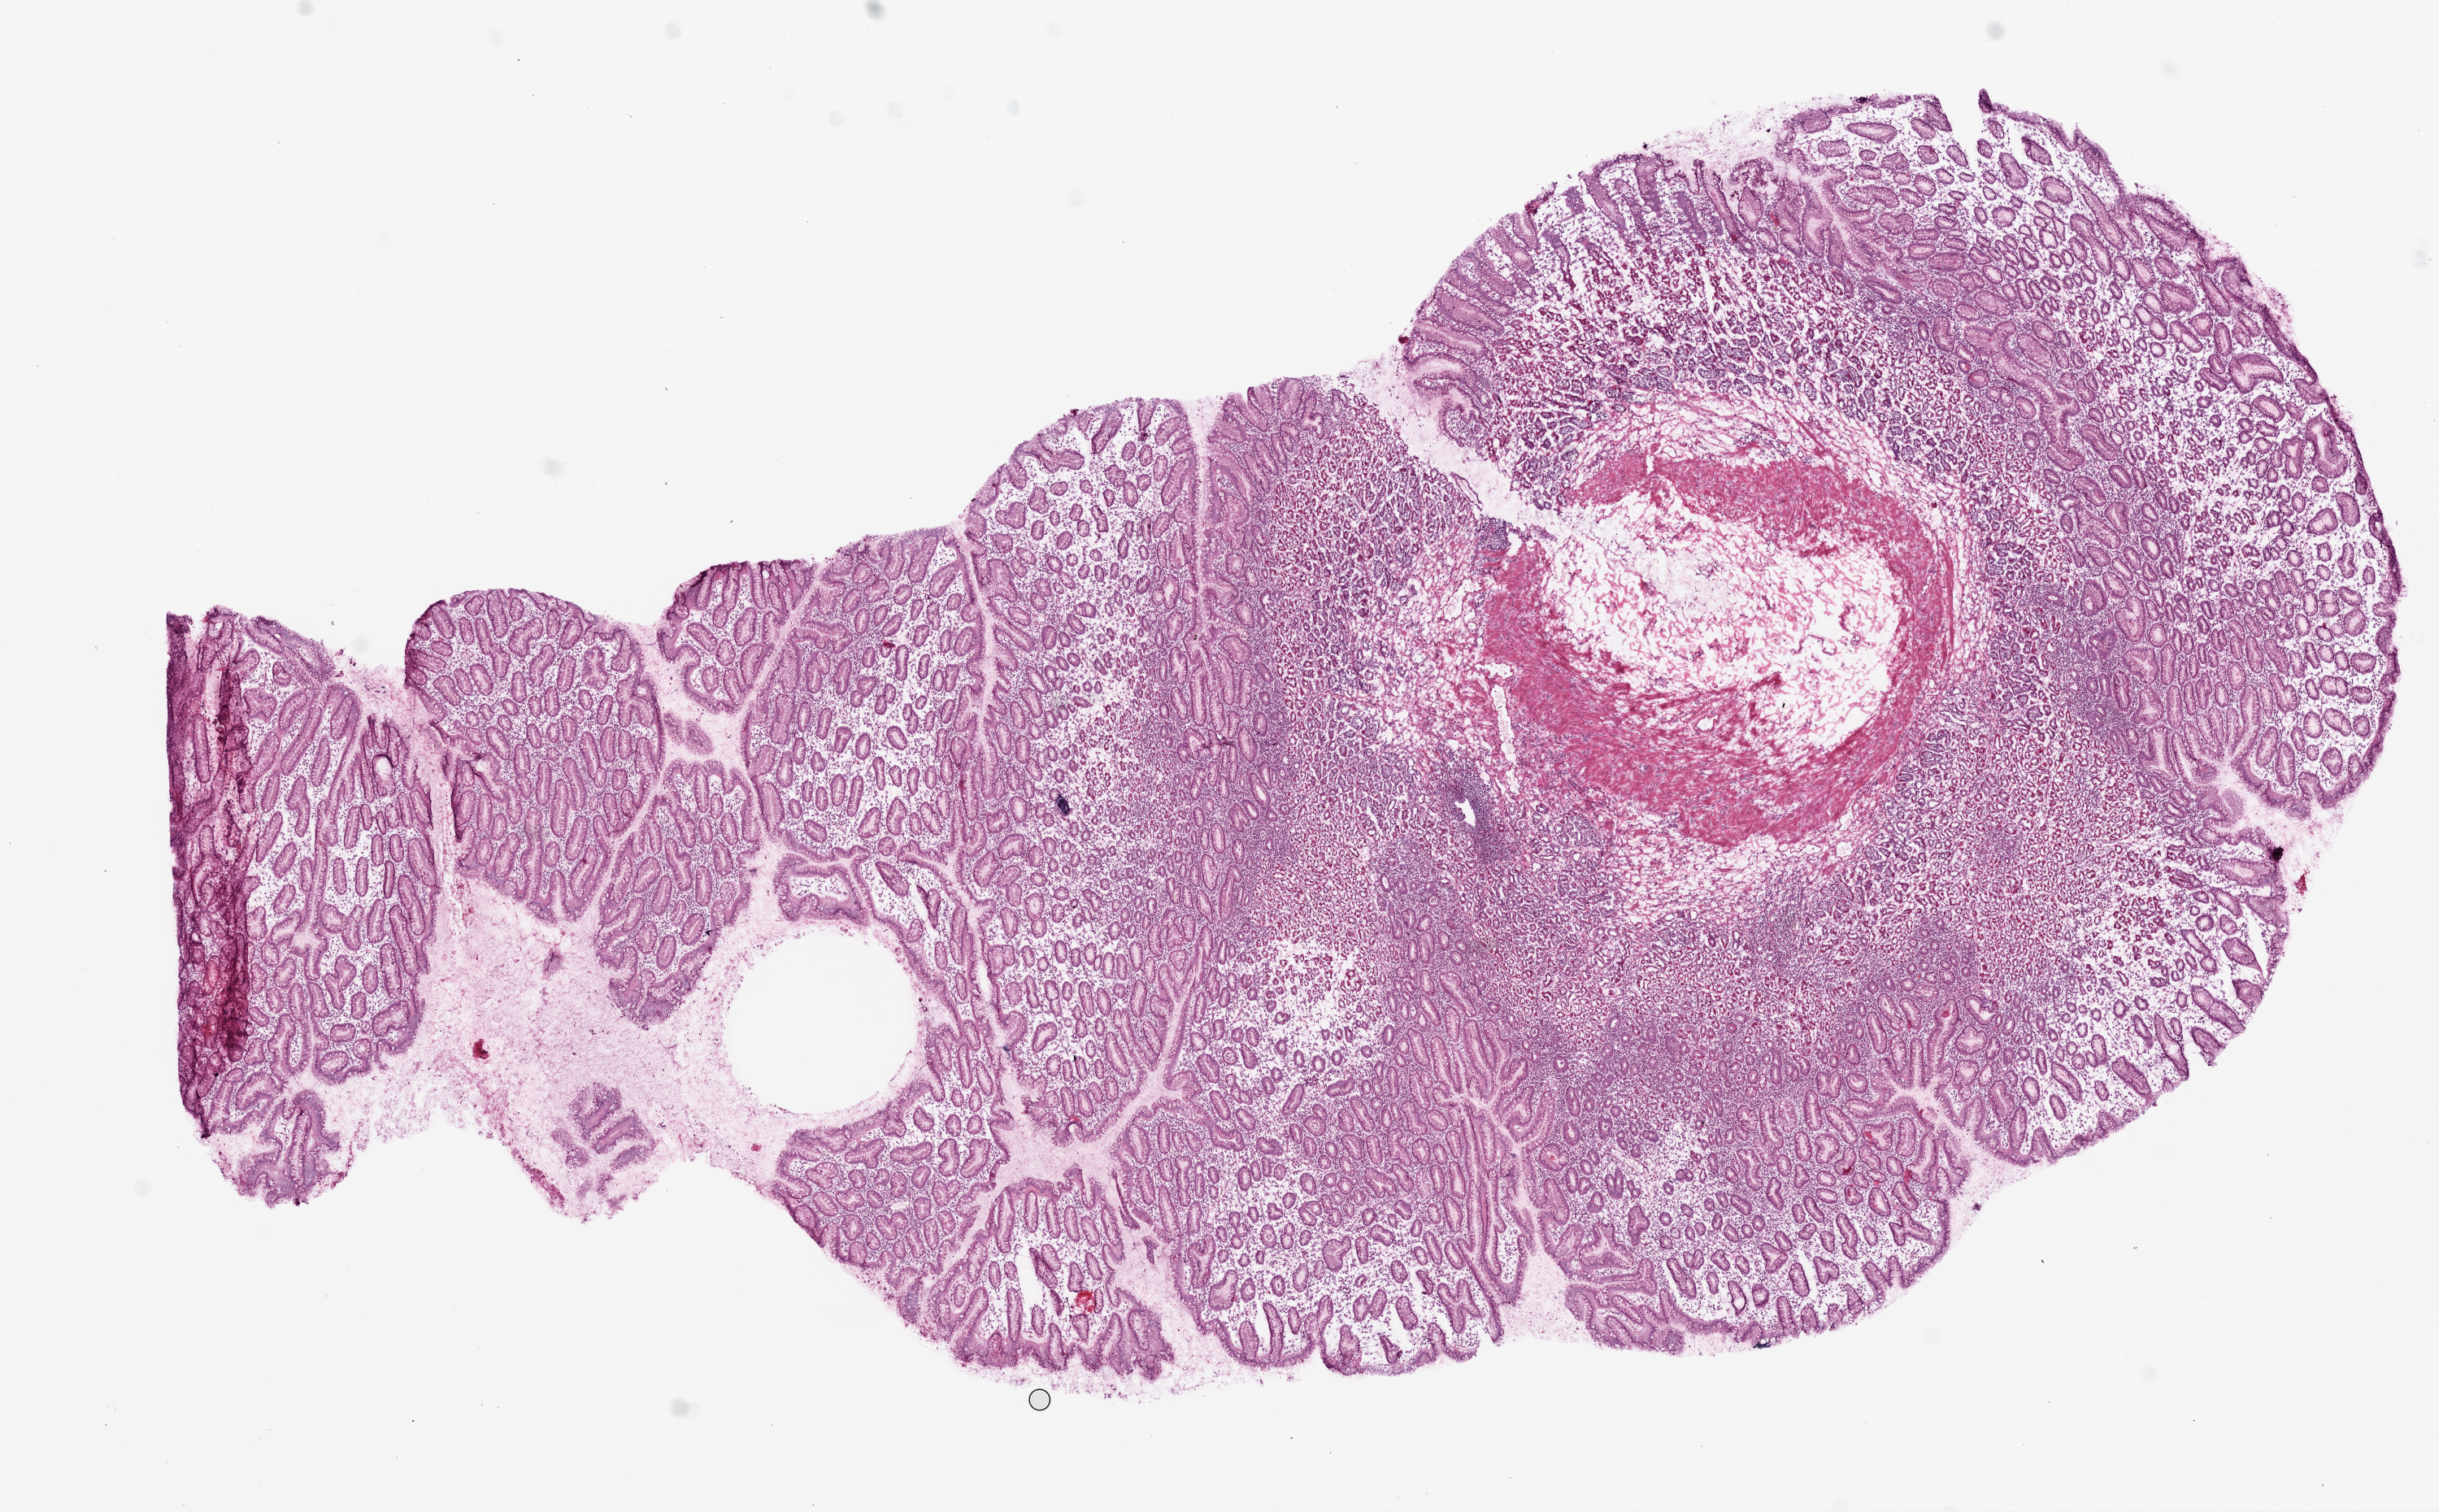
Digitized H&E tissue section (whole slide), whole scanned area (about 12.0 x 7.5 mm, acquisition: 20x scan) shown as a low-resolution overview. Frozen section from the top of the tissue portion. Sample: solid tissue normal (non-tumour tissue), stomach. Patient: male, age at initial diagnosis 65 years.
This section: solid tissue normal (non-tumour) sample from the same patient. Patient diagnosis: Tubular adenocarcinoma (body of stomach).